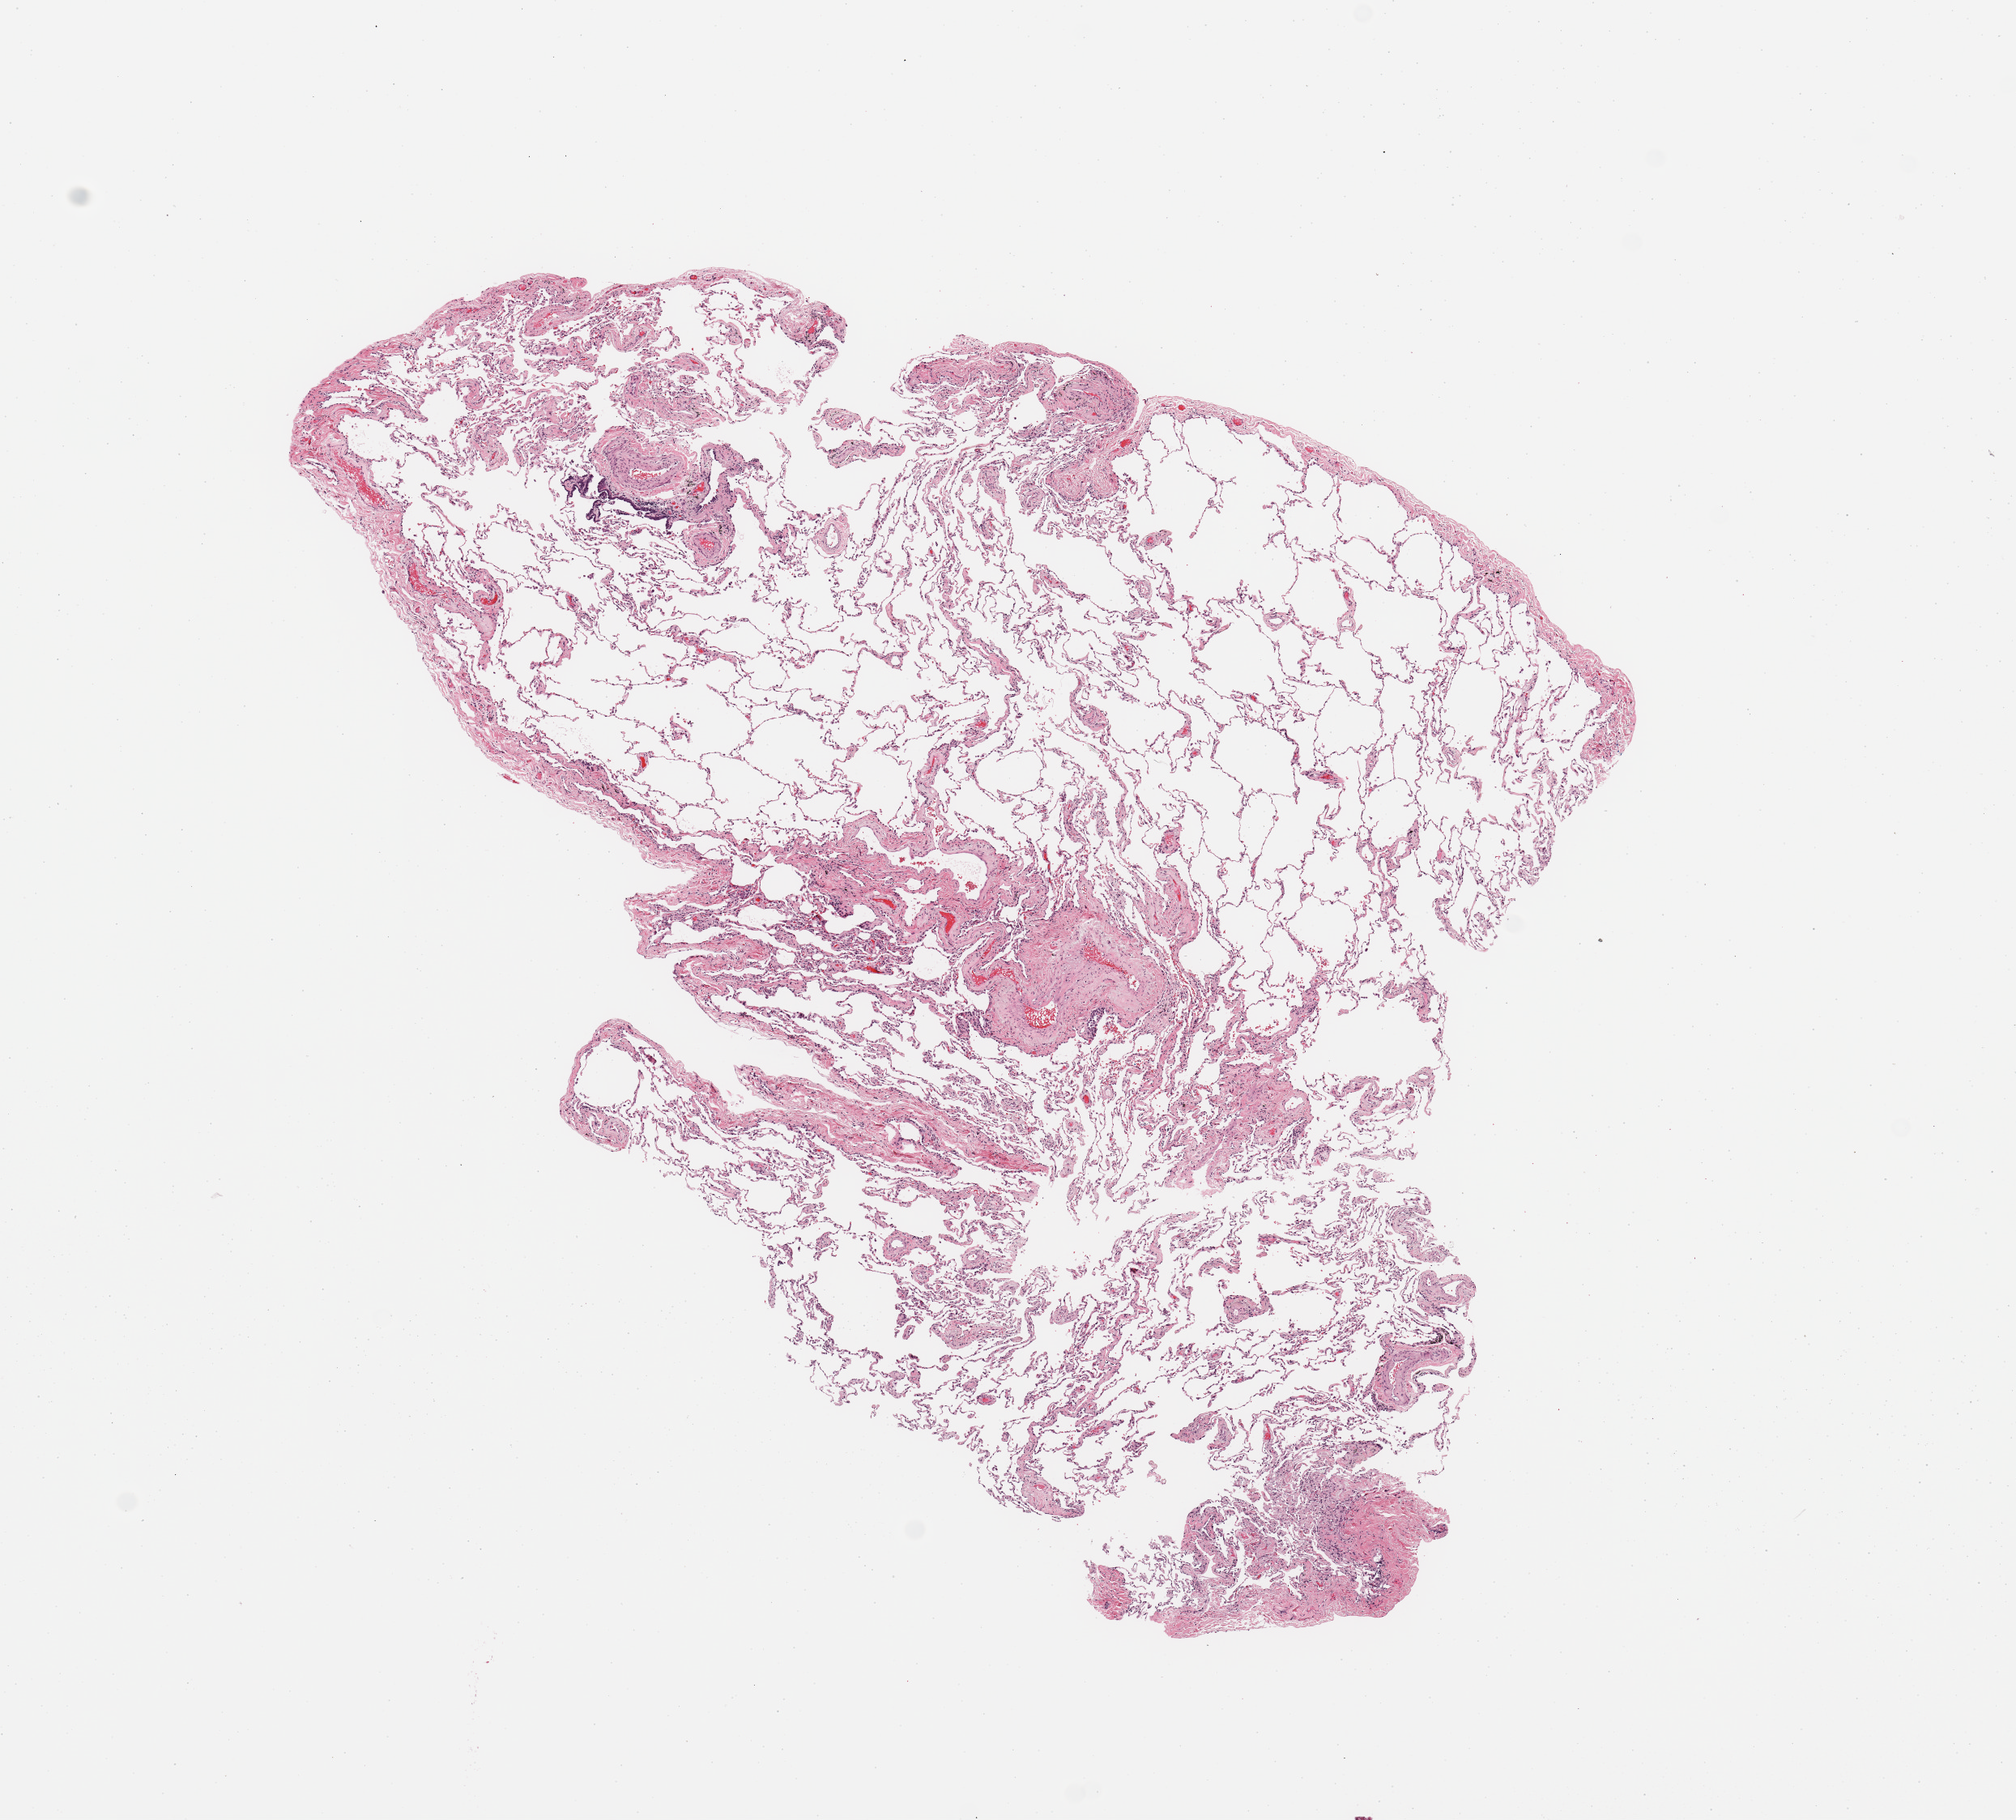
Digitized H&E tissue section (whole slide) — low-resolution overview of the scanned area, about 9.8 x 8.9 mm (slide scanned at 20x); normal (non-tumour) tissue sample, sampled site: lung. 74-year-old male patient.
- this section: normal (non-tumour) tissue from the same patient
- patient diagnosis: Squamous cell carcinoma, NOS